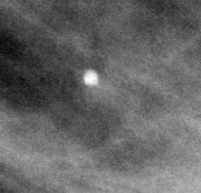
Cropped region of a digitized screen-film mammogram centred on a radiologist-marked abnormality, left breast, MLO view.
Finding: calcifications, morphology round and regular / lucent center; BI-RADS assessment category 2; subtlety rating 5 on a 1 (subtle) to 5 (obvious) scale; benign without callback (not worked up further).